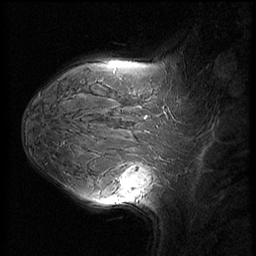
Breast MRI (dynamic contrast-enhanced), one sagittal slice; slice 43 of 60 in the series (ordered by position); dynamic contrast-enhanced series, image 2 of 3 at this slice position (ordered by acquisition); 1.5 T; TE 4.2 ms, TR 8.9 ms; 2.5 mm slice thickness; 256 × 256 image matrix, field of view 220 × 220 mm. Patient: female, 37 years. From the clinical record (not read from this slice): setting: breast cancer imaged before/during neoadjuvant chemotherapy; receptor status: triple-negative.
Structures marked on this image (semi-automatic segmentation, software-assisted and operator-edited):
- analysis volume of interest (the breast-tissue region the enhancement analysis was run in; not a lesion): bounding box [x1, y1, x2, y2] px = [114, 153, 159, 206]
- tumour enhancement mask (voxels above the 140 % enhancement threshold inside the analysis volume of interest): [122, 167, 153, 194]